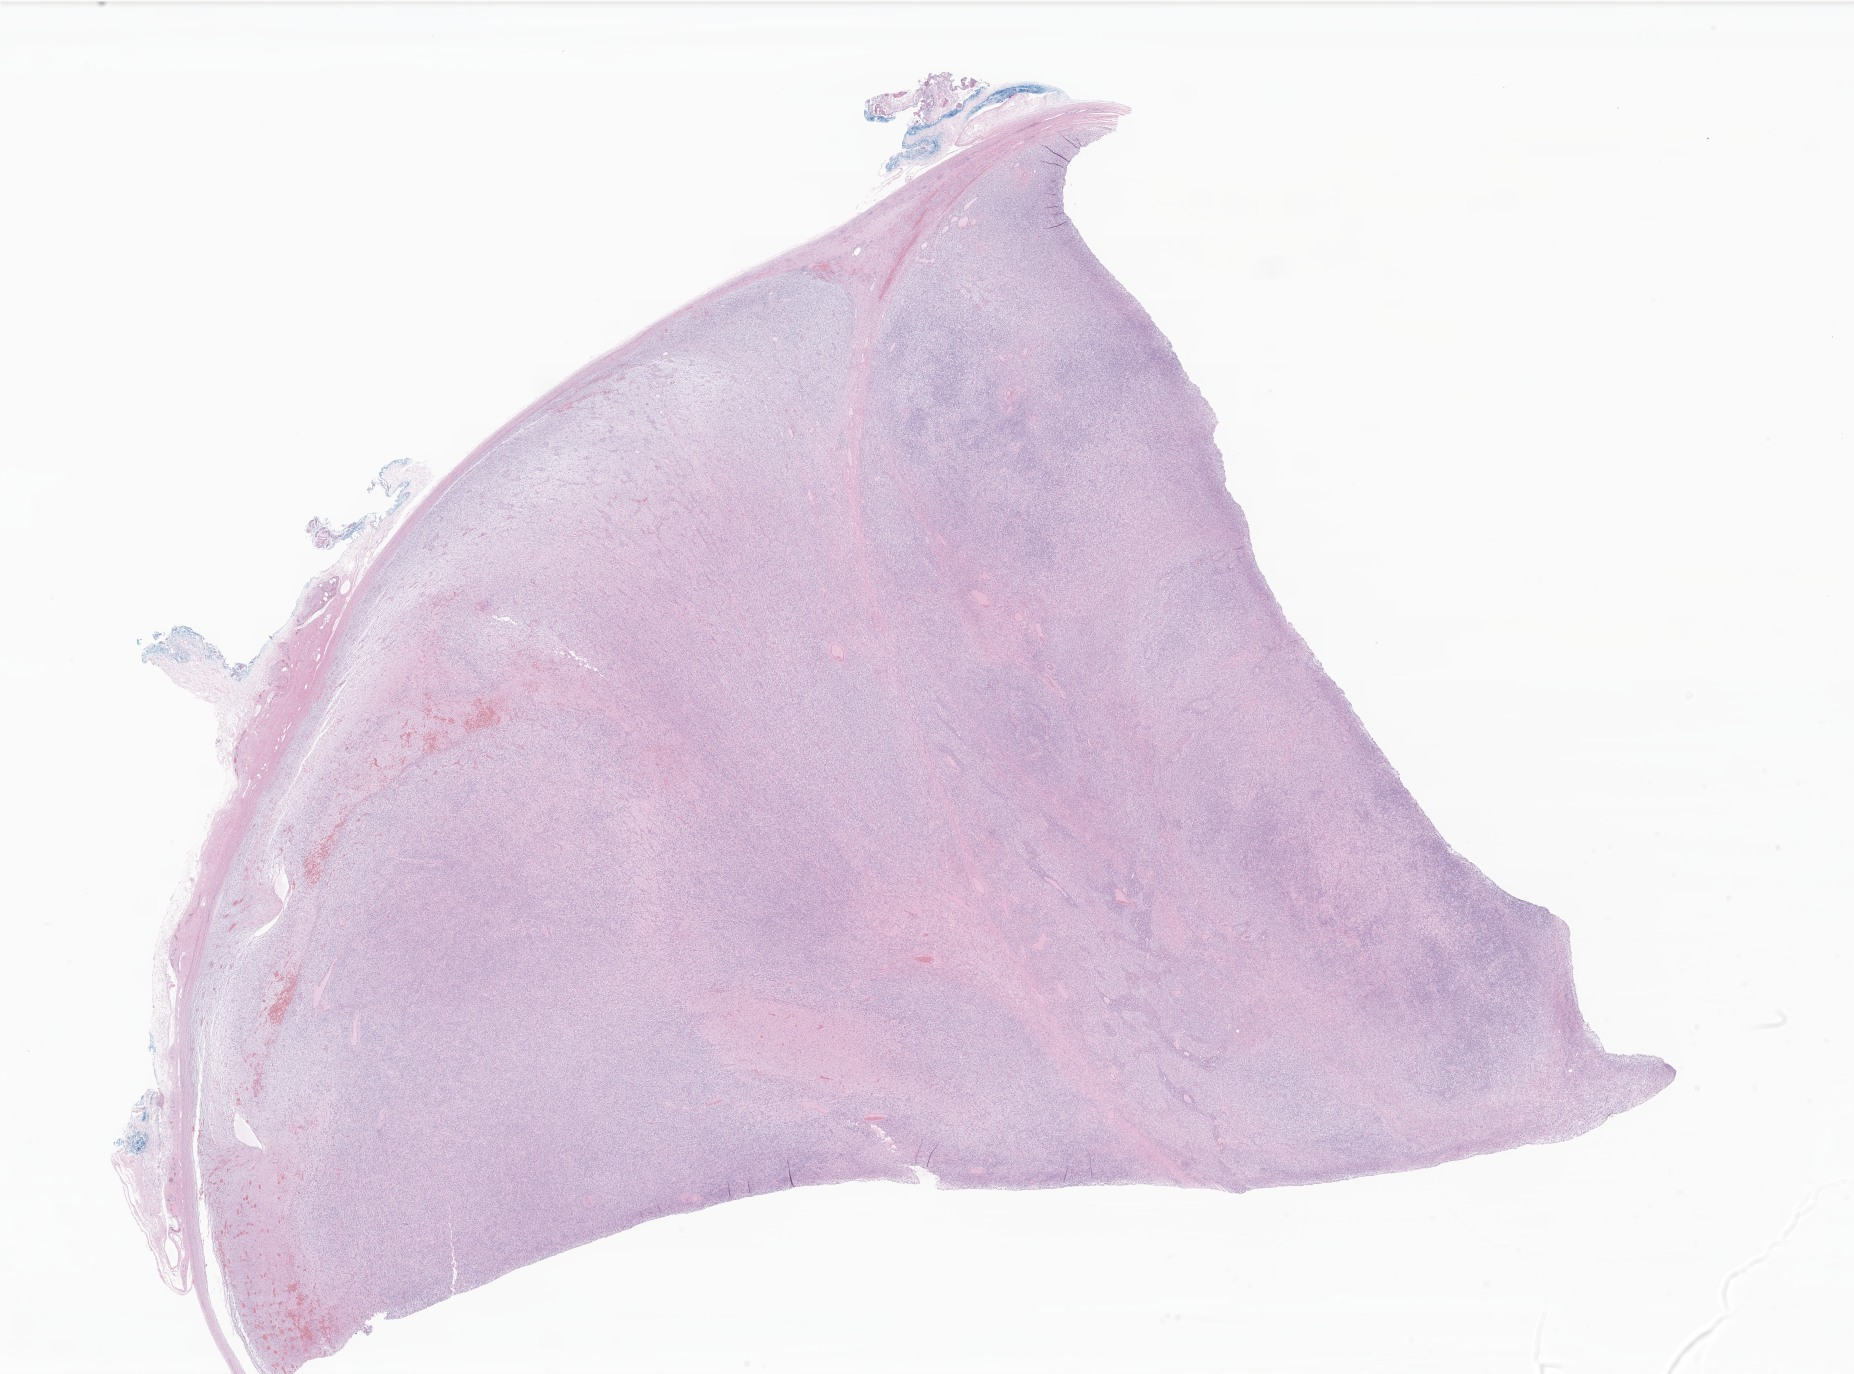
H&E whole-slide image of tumor tissue from the testis — low-resolution overview of the scanned area, about 31.3 x 23.2 mm. Formalin-fixed, paraffin-embedded (FFPE) tissue. Patient: male, age 159 months (13 years 3 months).
Diagnosis: Rhabdomyosarcoma, NOS.